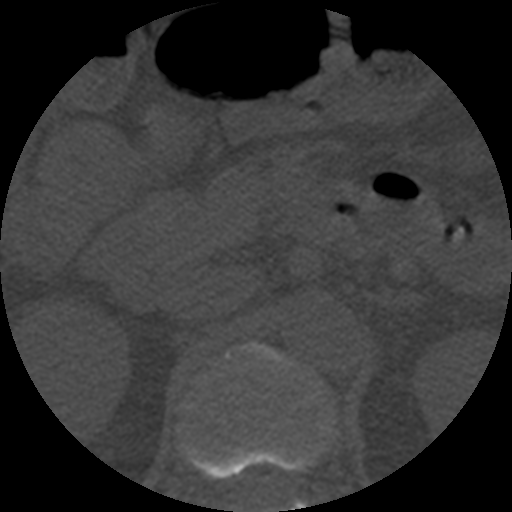
CT including the spine, one axial slice; slice 201 of 508 in the series (ordered by position); 120 kVp; bone window (W 1800 / L 400 HU); 512 × 512 image matrix. Patient age 57 years. From the clinical record (not read from this slice): primary cancer: prostate.
Outlined on this slice (semi-automatic segmentation, software-assisted and operator-edited):
- L1 vertebra: bounding box [x1, y1, x2, y2] px = [243, 344, 306, 512]
- T12 vertebra: [182, 443, 316, 479]